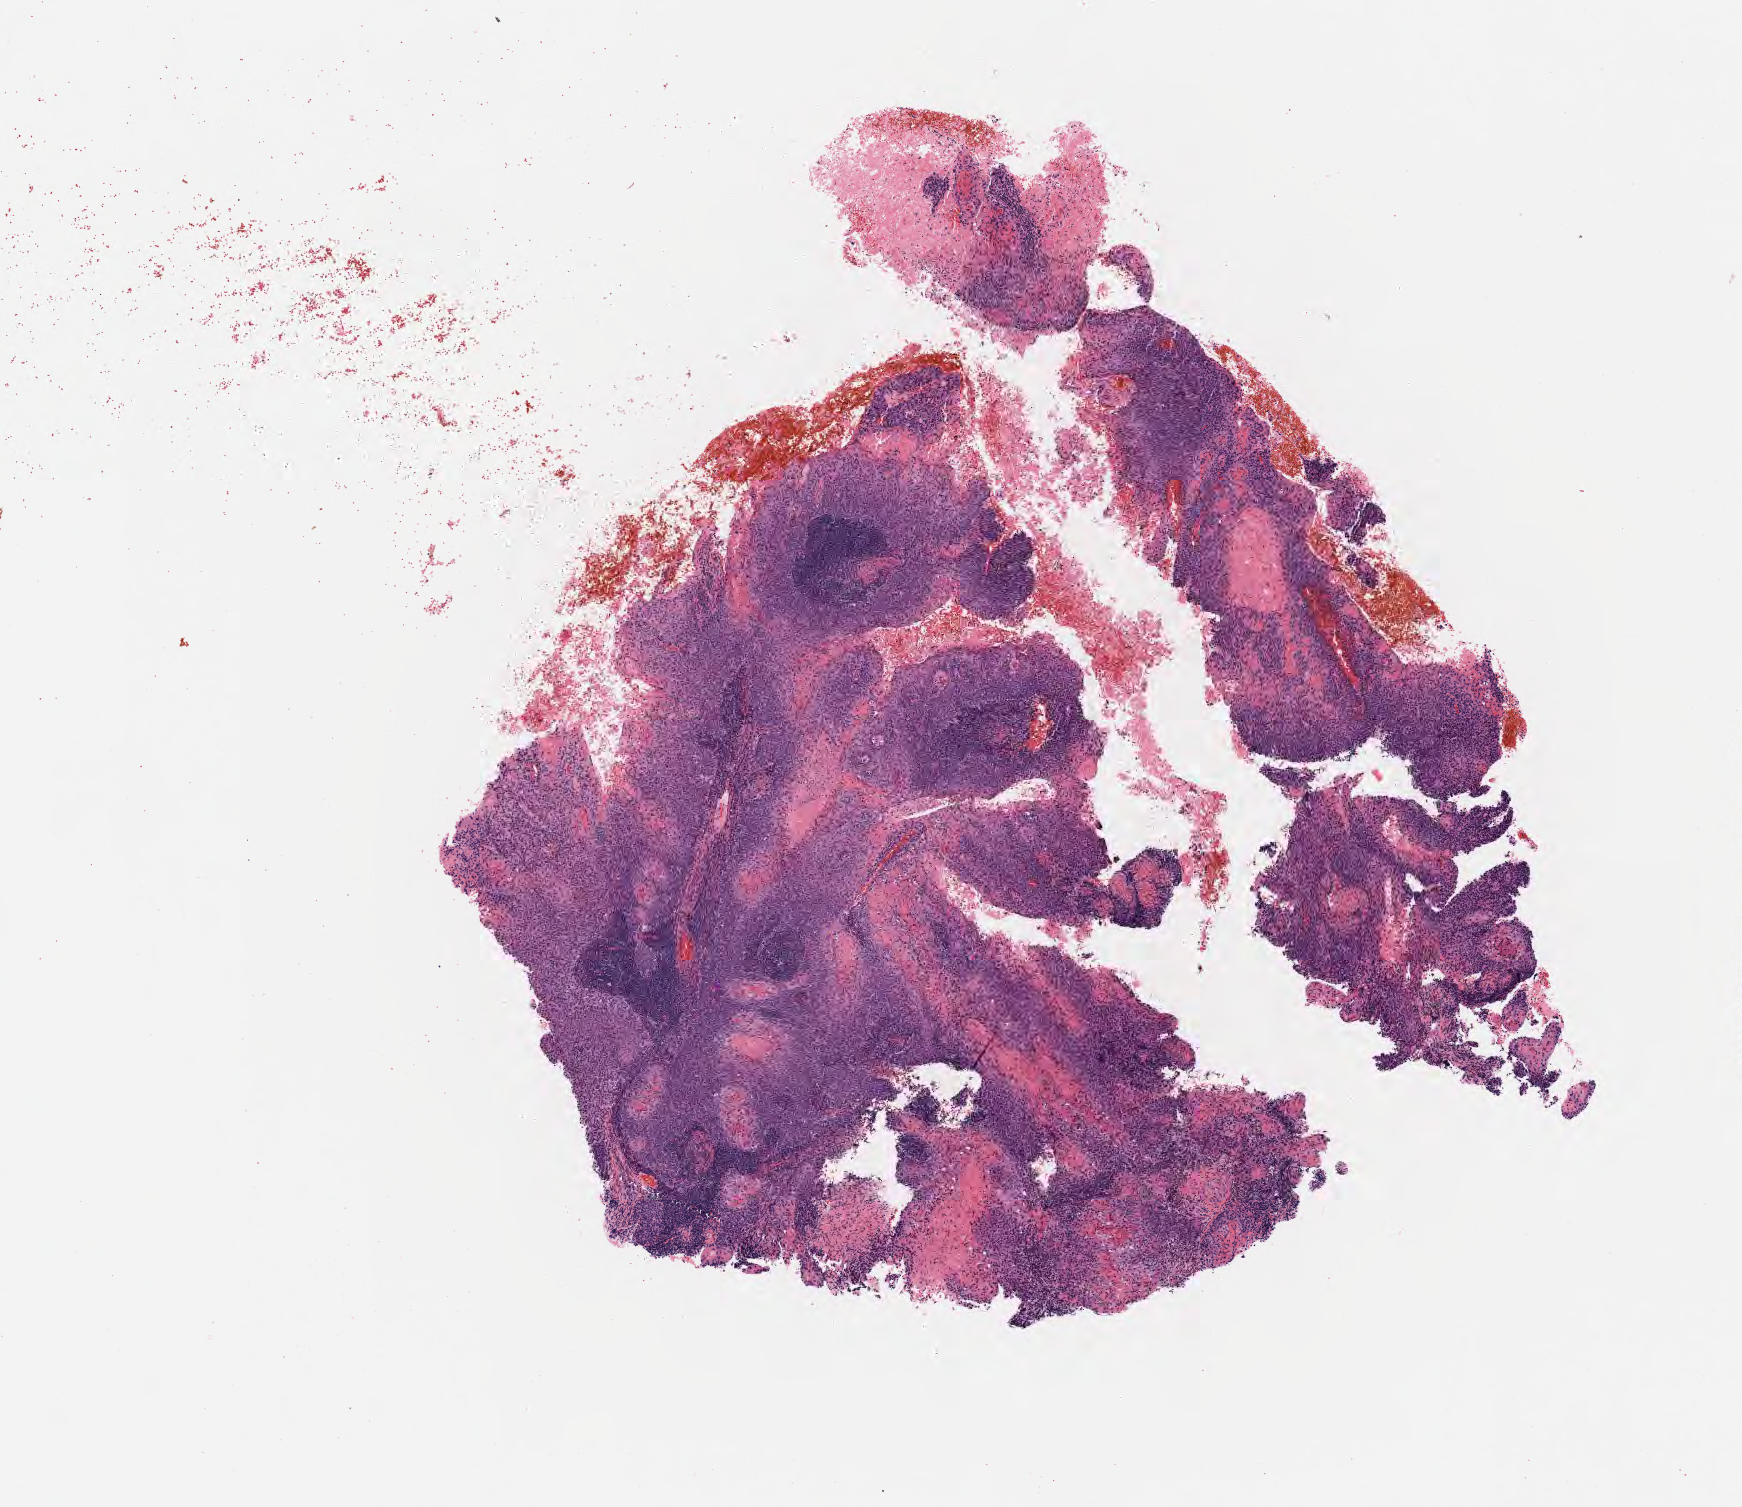
Haematoxylin and eosin whole-slide image — a low-resolution overview of the entire scanned area, about 7.0 x 6.1 mm; specimen: tumor tissue; anatomic site: cervix. Female patient, 56 years old.
* diagnosis: Squamous cell carcinoma, keratinizing, NOS